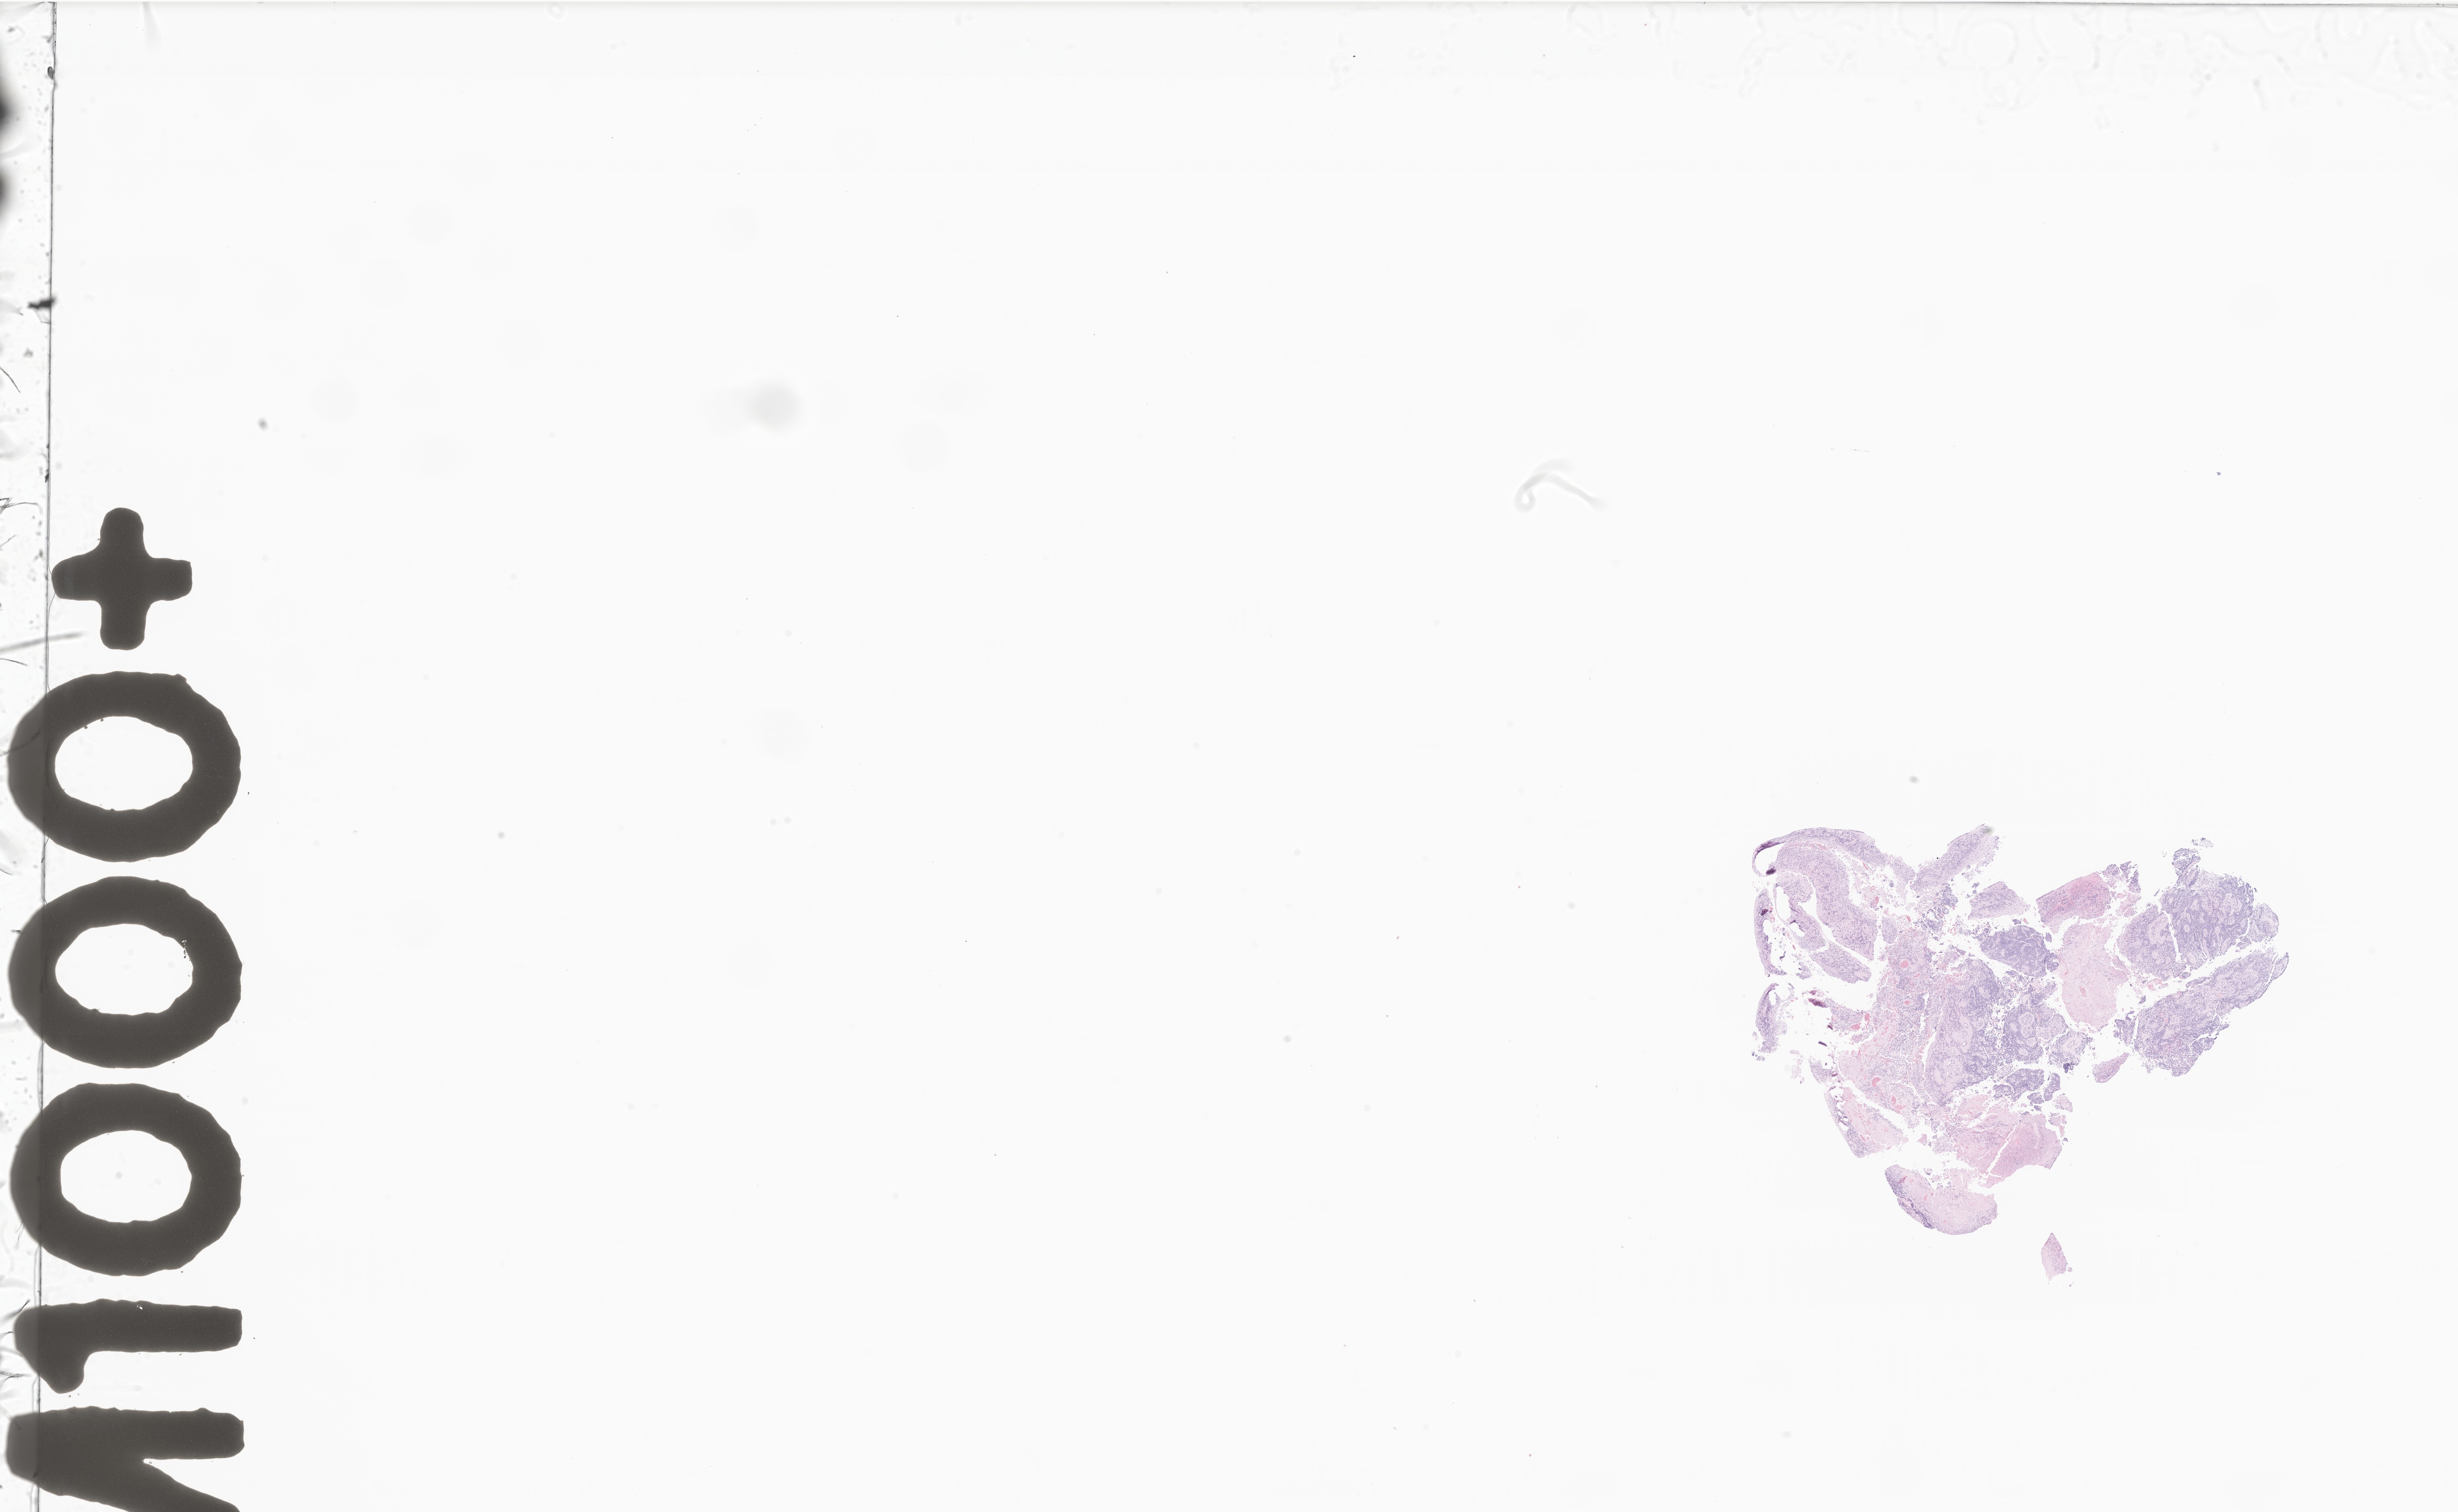
Hematoxylin and eosin (H&E) whole-slide image of tumor tissue from the cerebellum, shown as a low-resolution overview of the whole scanned area (about 27.4 x 16.8 mm), FFPE section. Male patient, age 87 months.
• diagnosis: Ependymoma, NOS